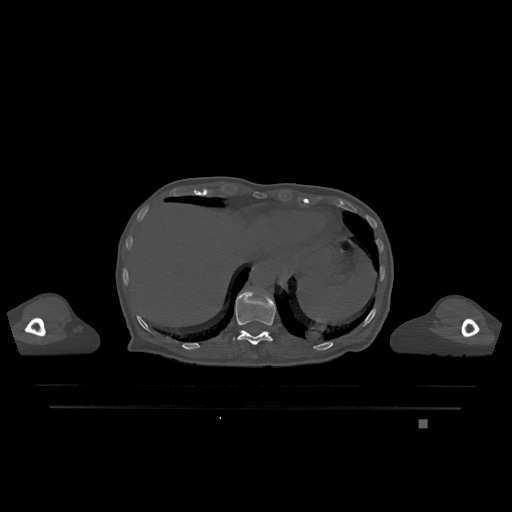
CT including the spine, one axial slice; position 585 of 1317 along the scan axis; bone window (W 1800 / L 400 HU); 0.5 mm slice thickness; 512 × 512 image matrix, field of view 500 × 500 mm. Female patient, age 74 years. From the clinical record (not read from this slice): primary cancer: lung; vertebrae with lytic lesions (as recorded): T1, T4, T5, T6, L4, L5.
Structures marked on this image (semi-automatic segmentation, software-assisted and operator-edited):
- T11 vertebra: bounding box (x1, y1, x2, y2) in pixels: (233, 289, 276, 345)